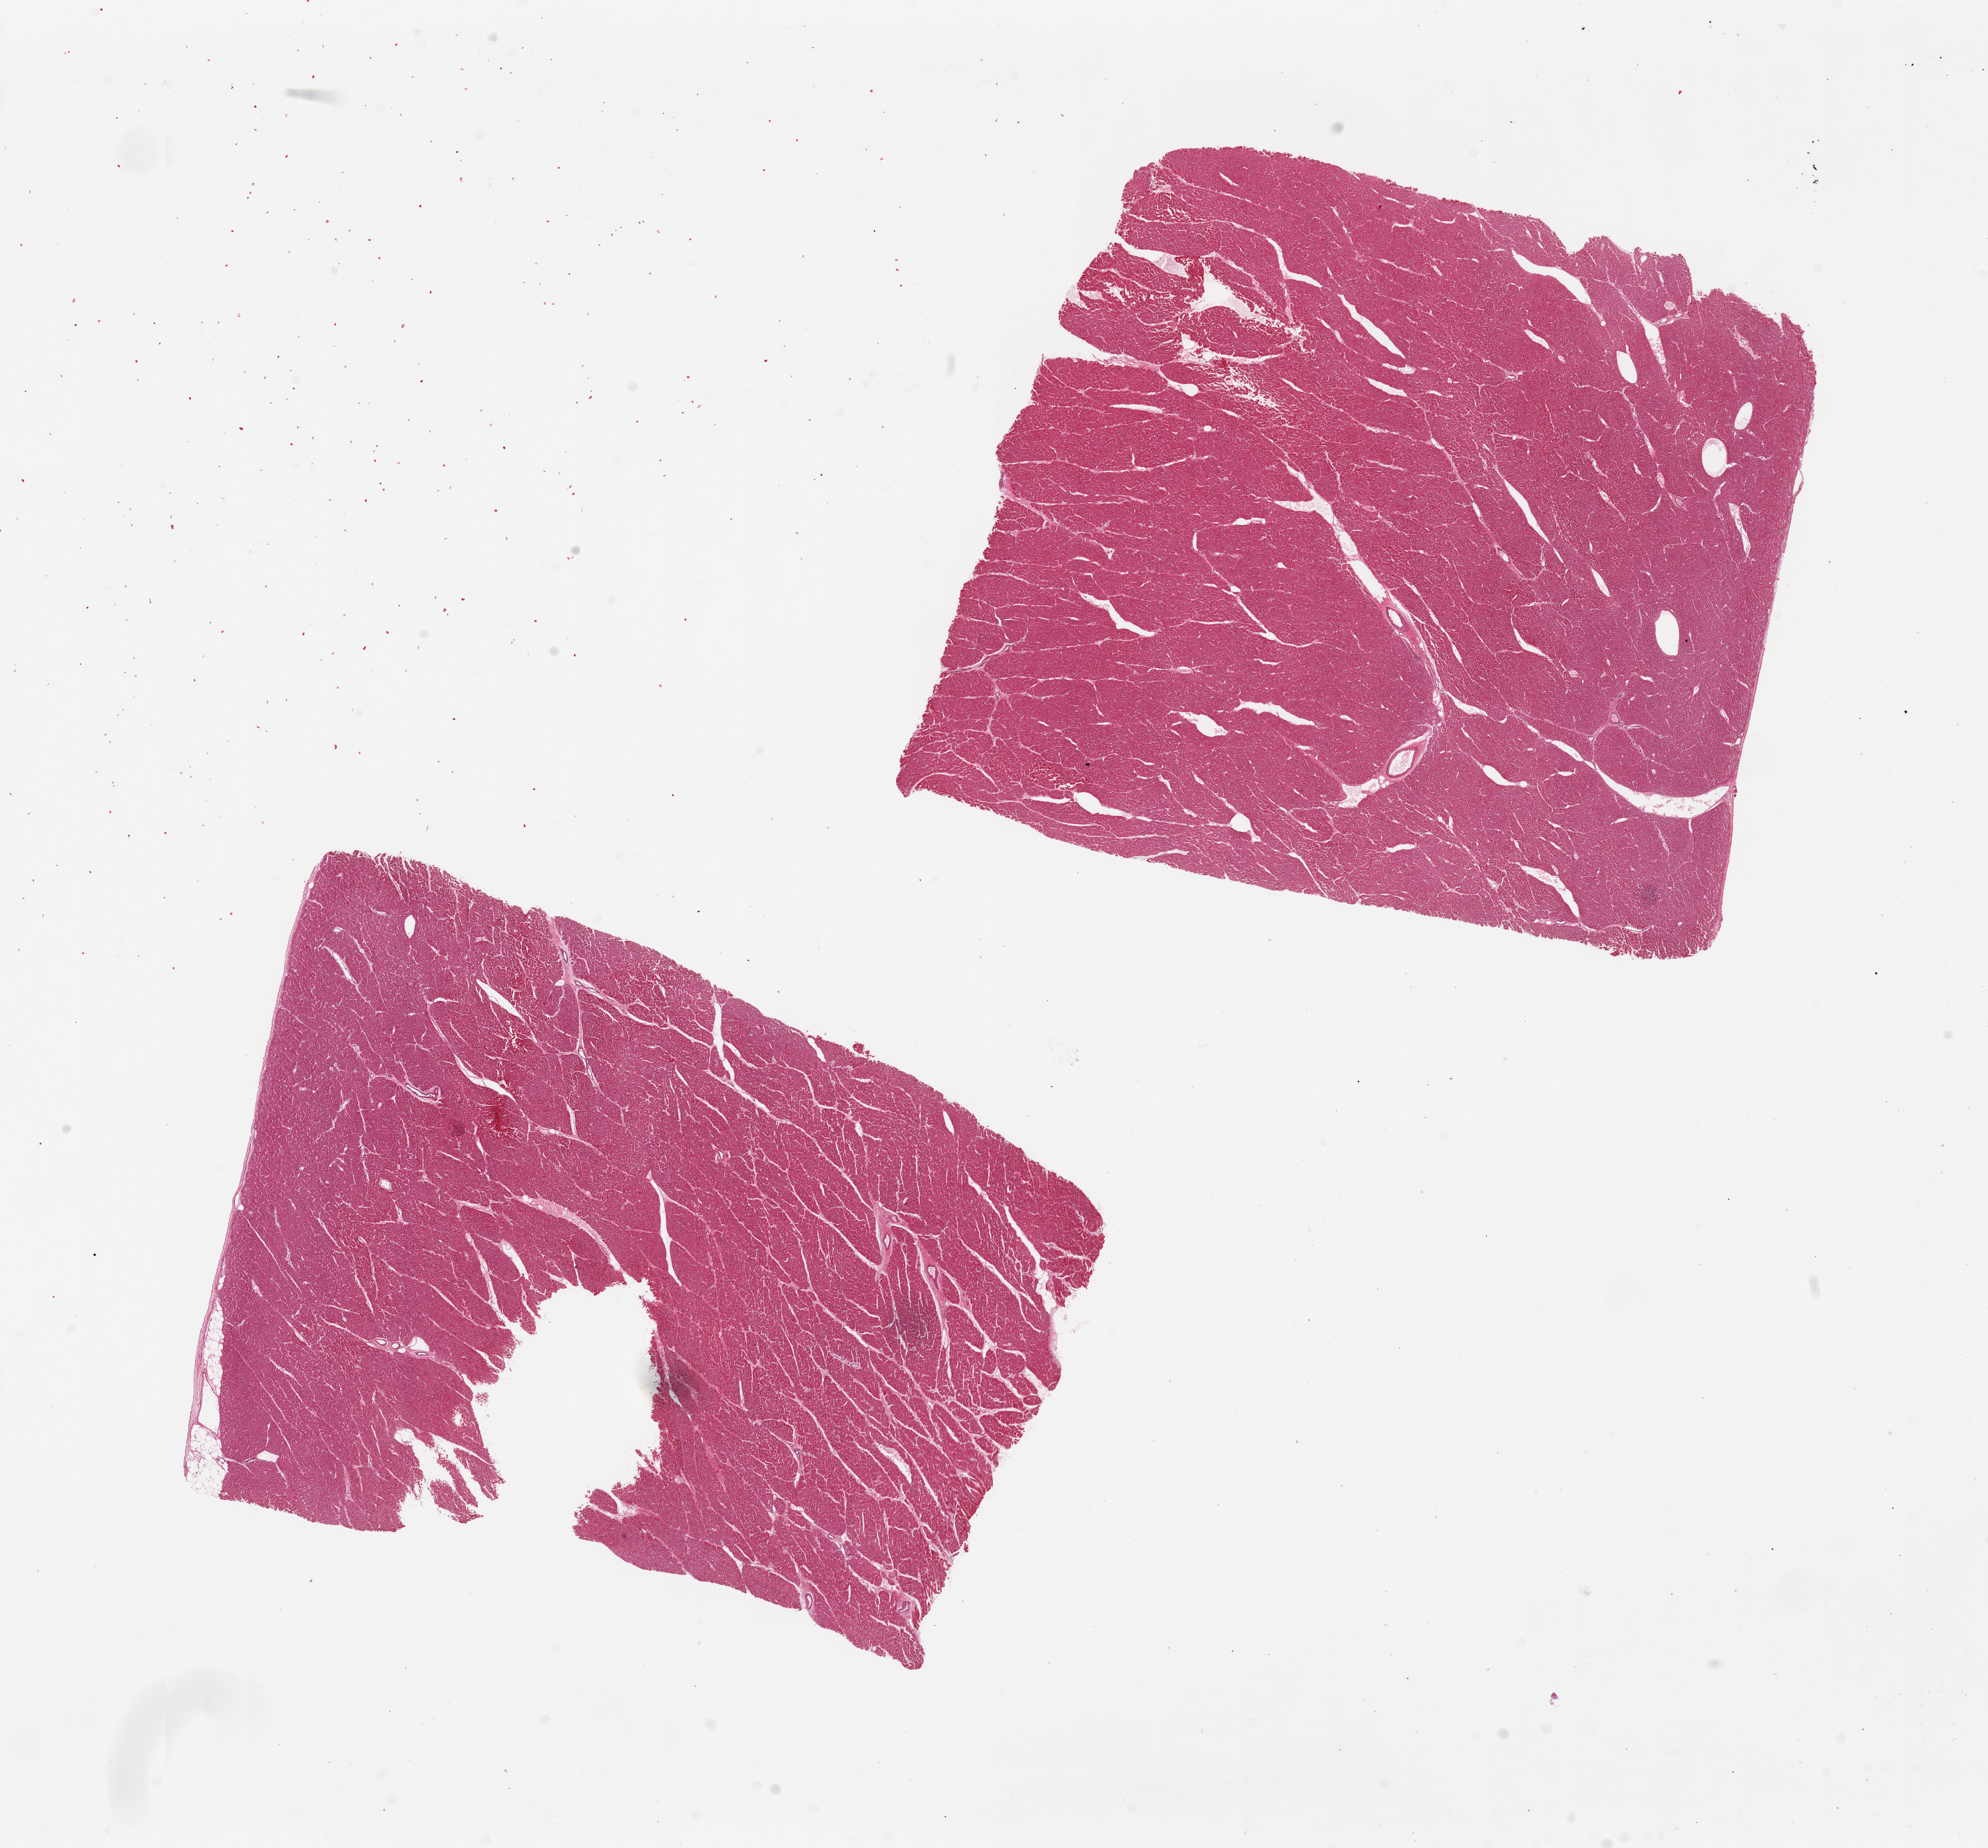
Whole-slide image, haematoxylin and eosin stain, a low-resolution overview of the entire scanned area, about 23.6 x 22.0 mm. PAXgene-fixed paraffin-embedded (PFPE) section. Sampled site (target tissue): heart. Tissue donor sample.
Pathologist's review note for this sample: 2 pieces, 11x8 & 10x8mm. 2x3 mm artifactual defect in 1 piece.